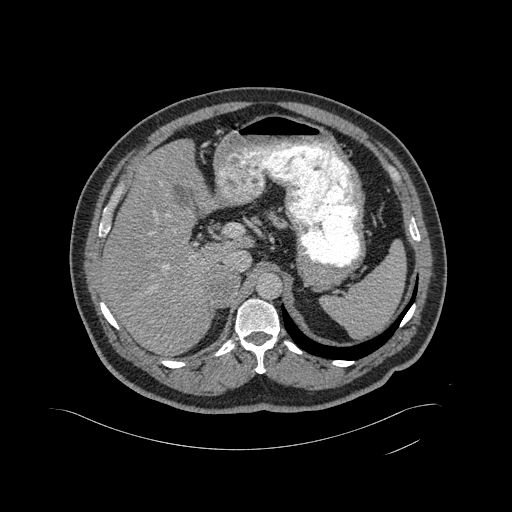
Contrast-enhanced abdominal CT, one axial slice. Position 330 of 433 along the scan axis. 120 kVp. Intravenous contrast given. Soft-tissue window (W 400 / L 40 HU). 512 × 512 image matrix, field of view 500 × 500 mm. Patient: male, 56 years. From the clinical record (not read from this slice): diagnosis: adrenocortical carcinoma; tumour side: right adrenal; tumour size at pathology: 11.6 cm; Ki-67 index: 50 %; stage (as recorded): 3.
Outlined on this slice (semi-automatic segmentation, software-assisted and operator-edited):
- mass: bounding box (x1, y1, x2, y2) in pixels: (207, 266, 239, 306)